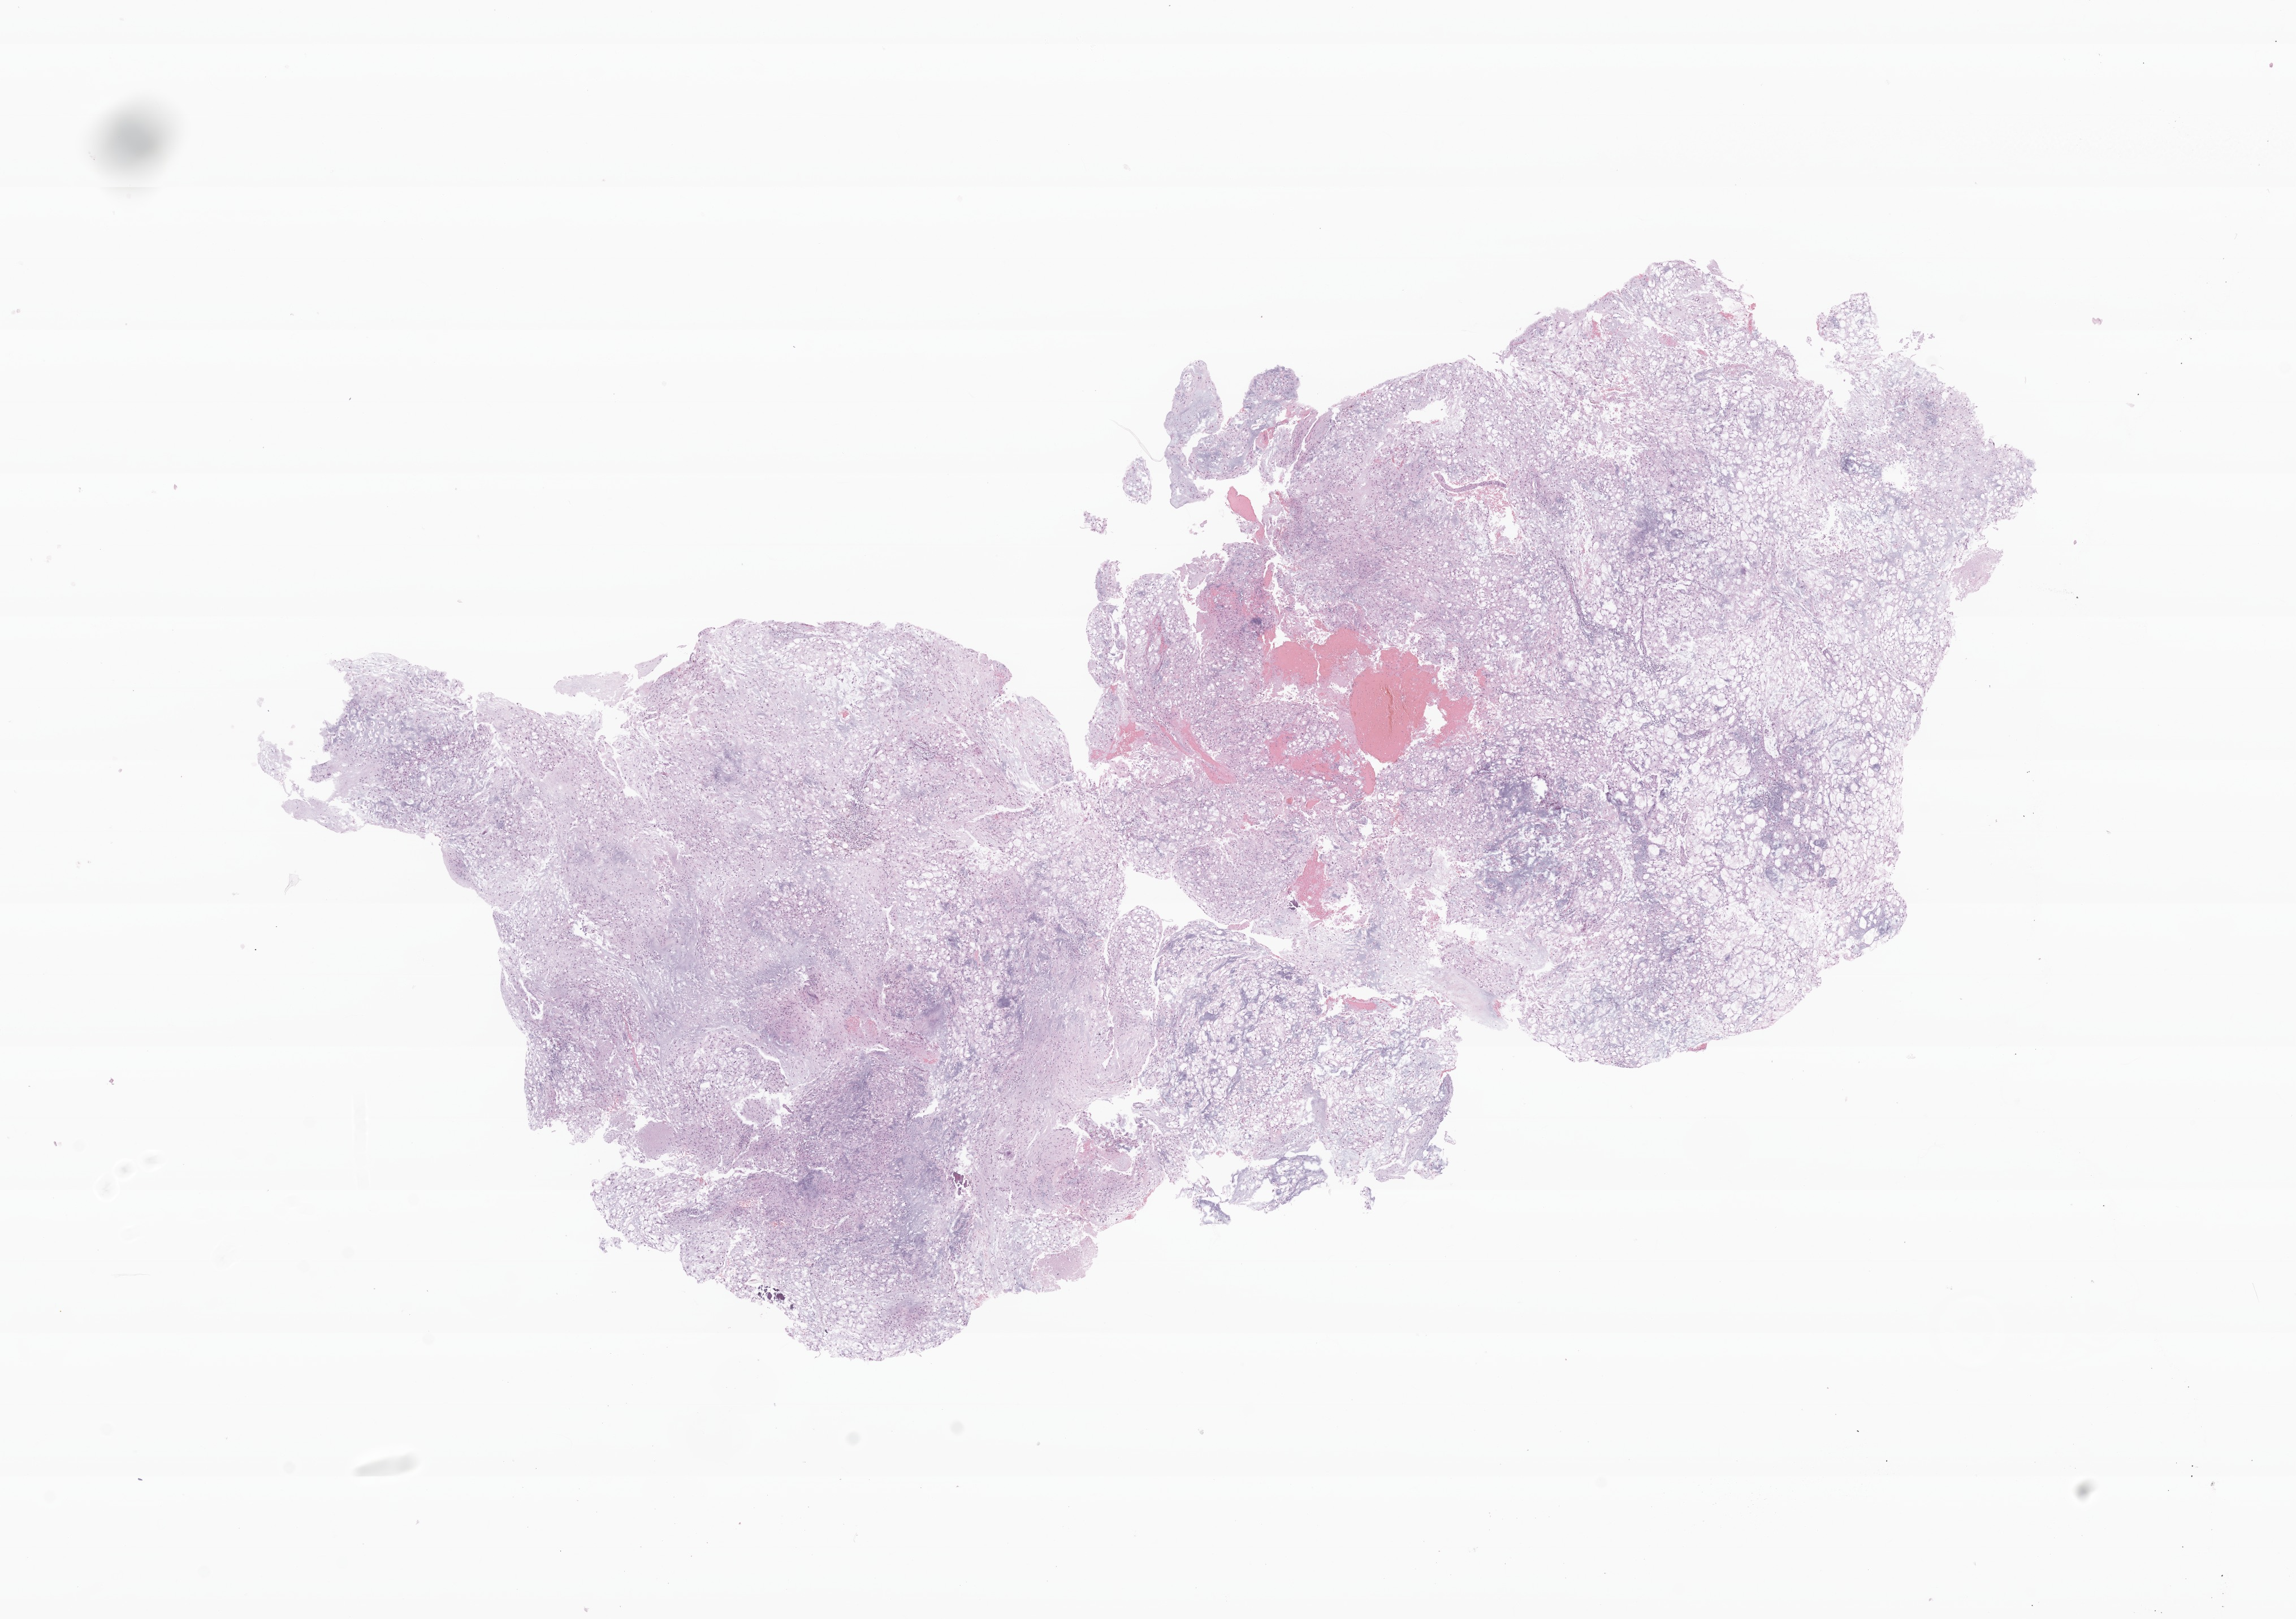
H&E whole-slide image of tumor tissue from the brain — a low-resolution overview of the entire scanned area, about 17.1 x 12.0 mm, formalin-fixed, paraffin-embedded (FFPE) tissue. Patient: female, age 129 months (10 years 9 months).
* recorded diagnosis: Tumor cells, malignant